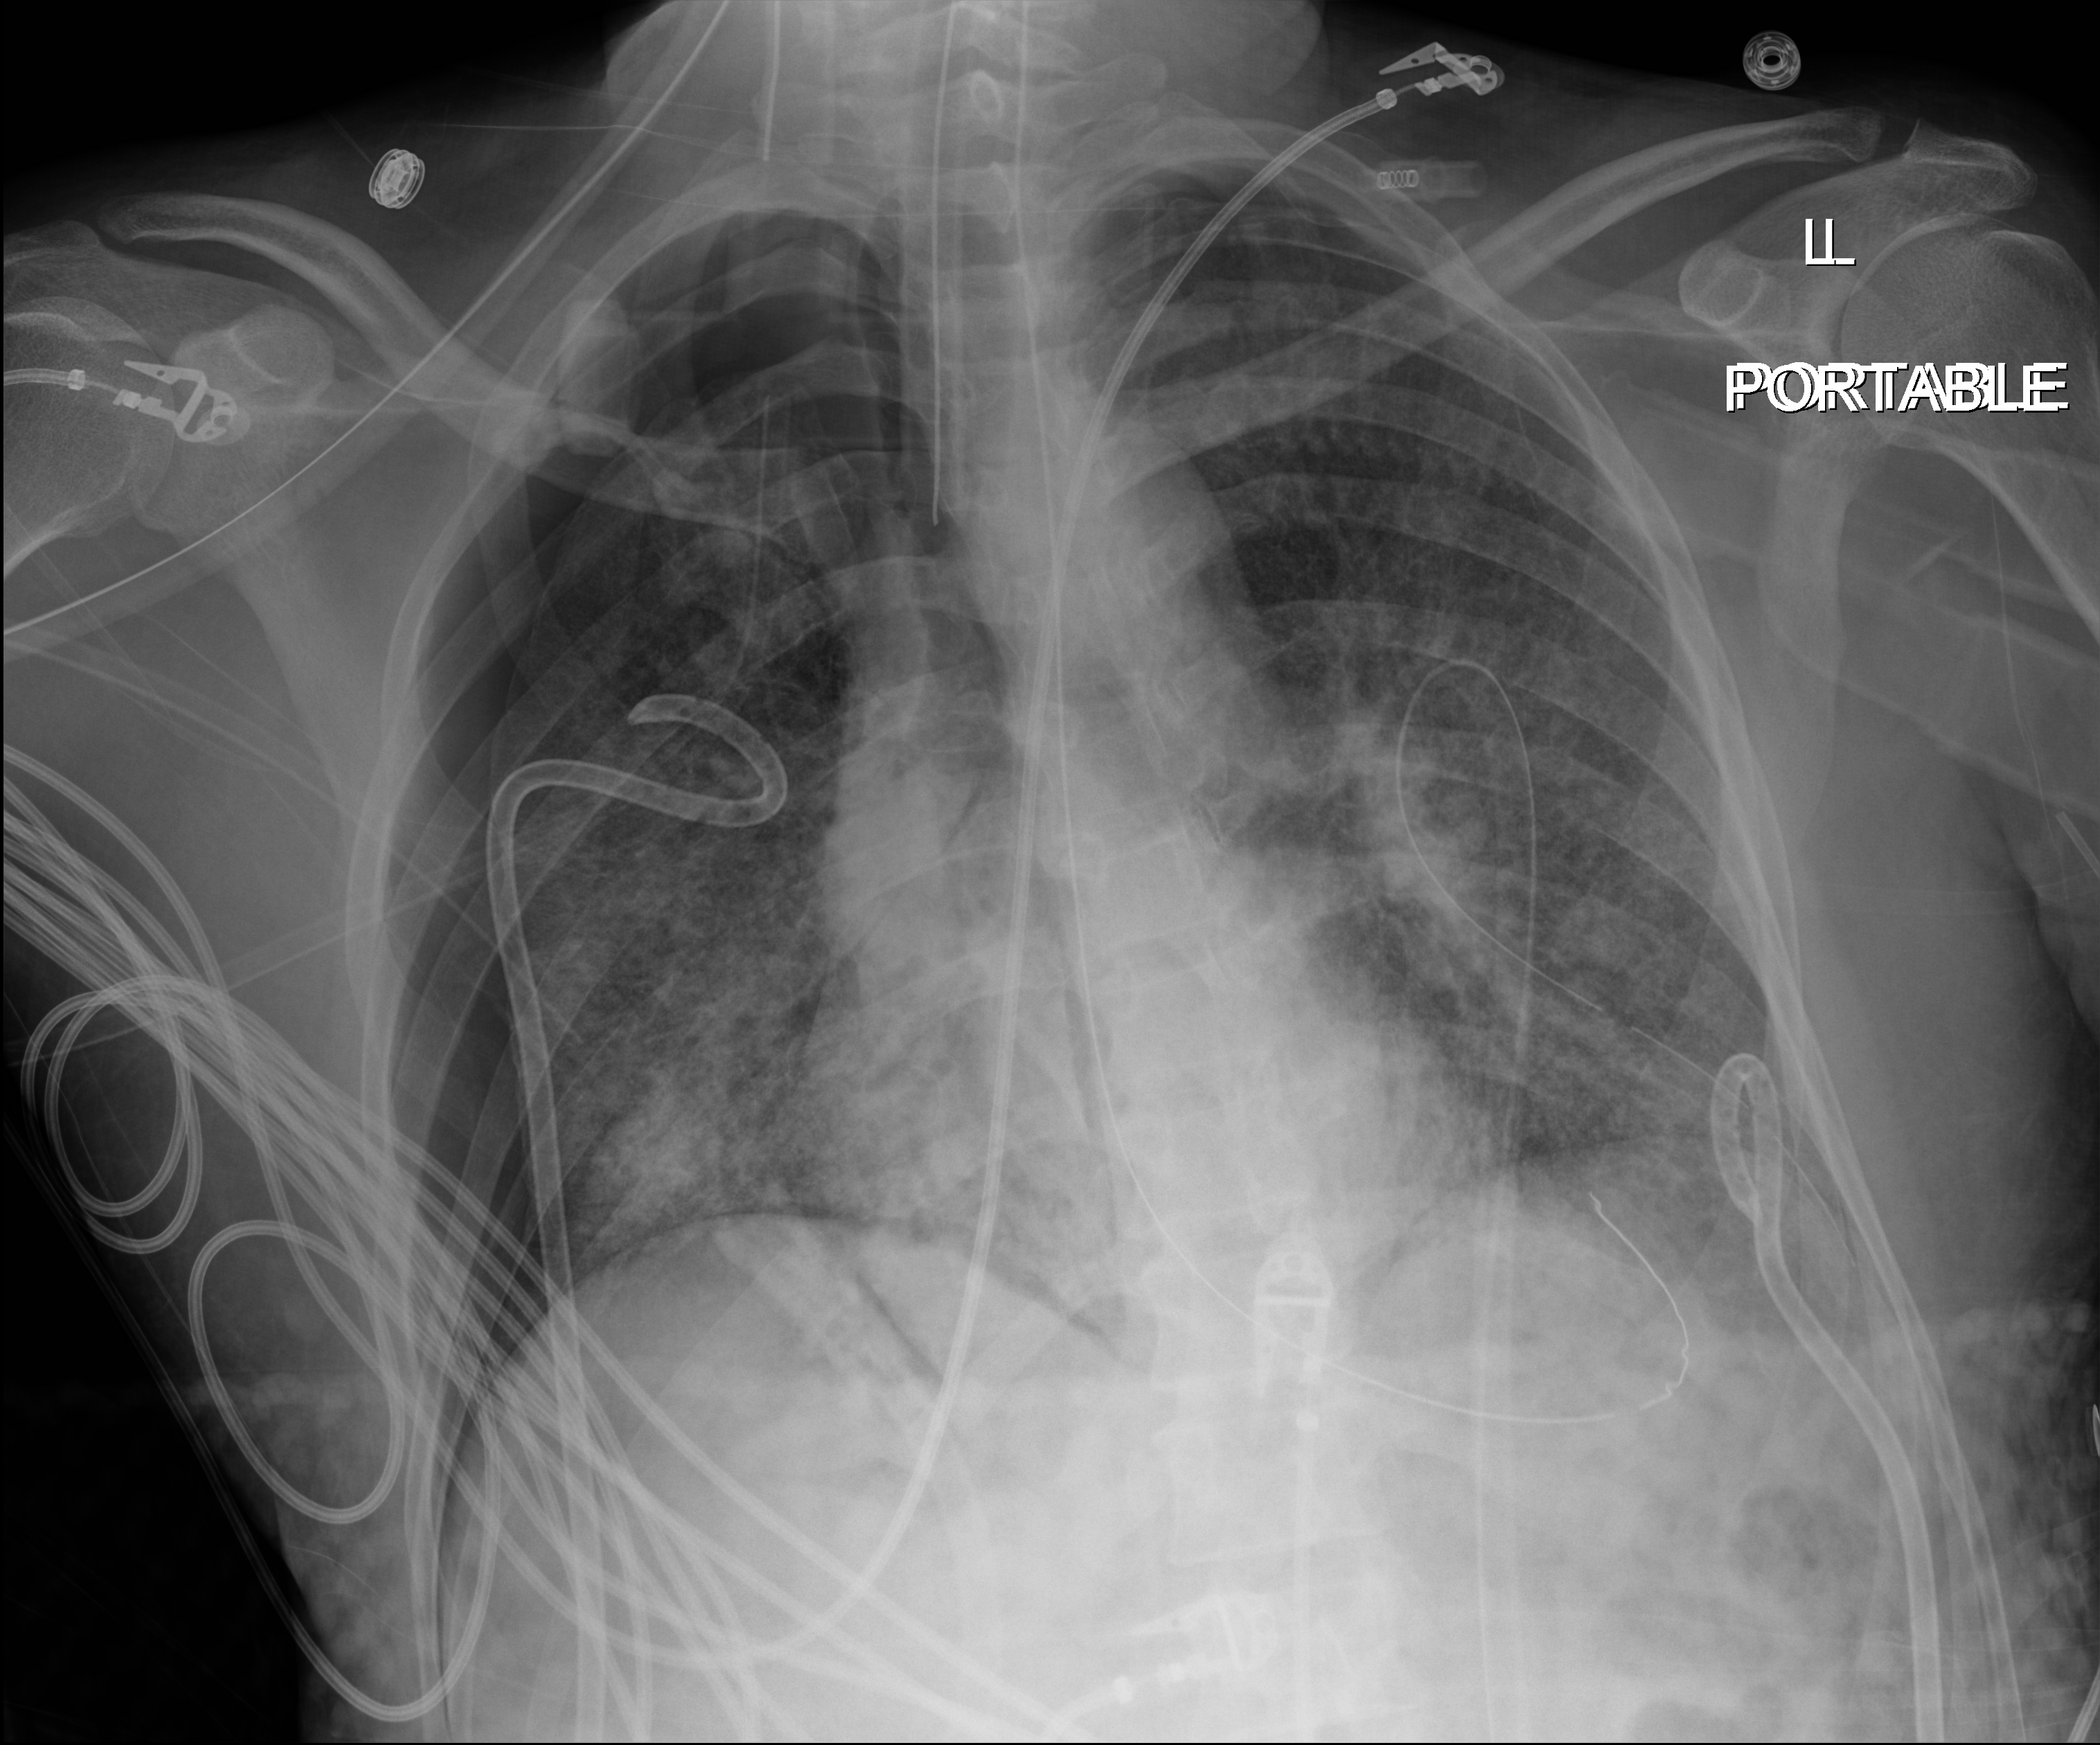
Bedside chest radiograph (digital radiography), anteroposterior (AP) projection. Patient hospitalised with COVID-19, aged 18–59 years.
Hospital-stay facts (about this admission, not read from this image; timing relative to this image not recorded):
- diabetes (admission record): no
- mechanically ventilated during this hospital stay: yes
- smoking status (admission record): never